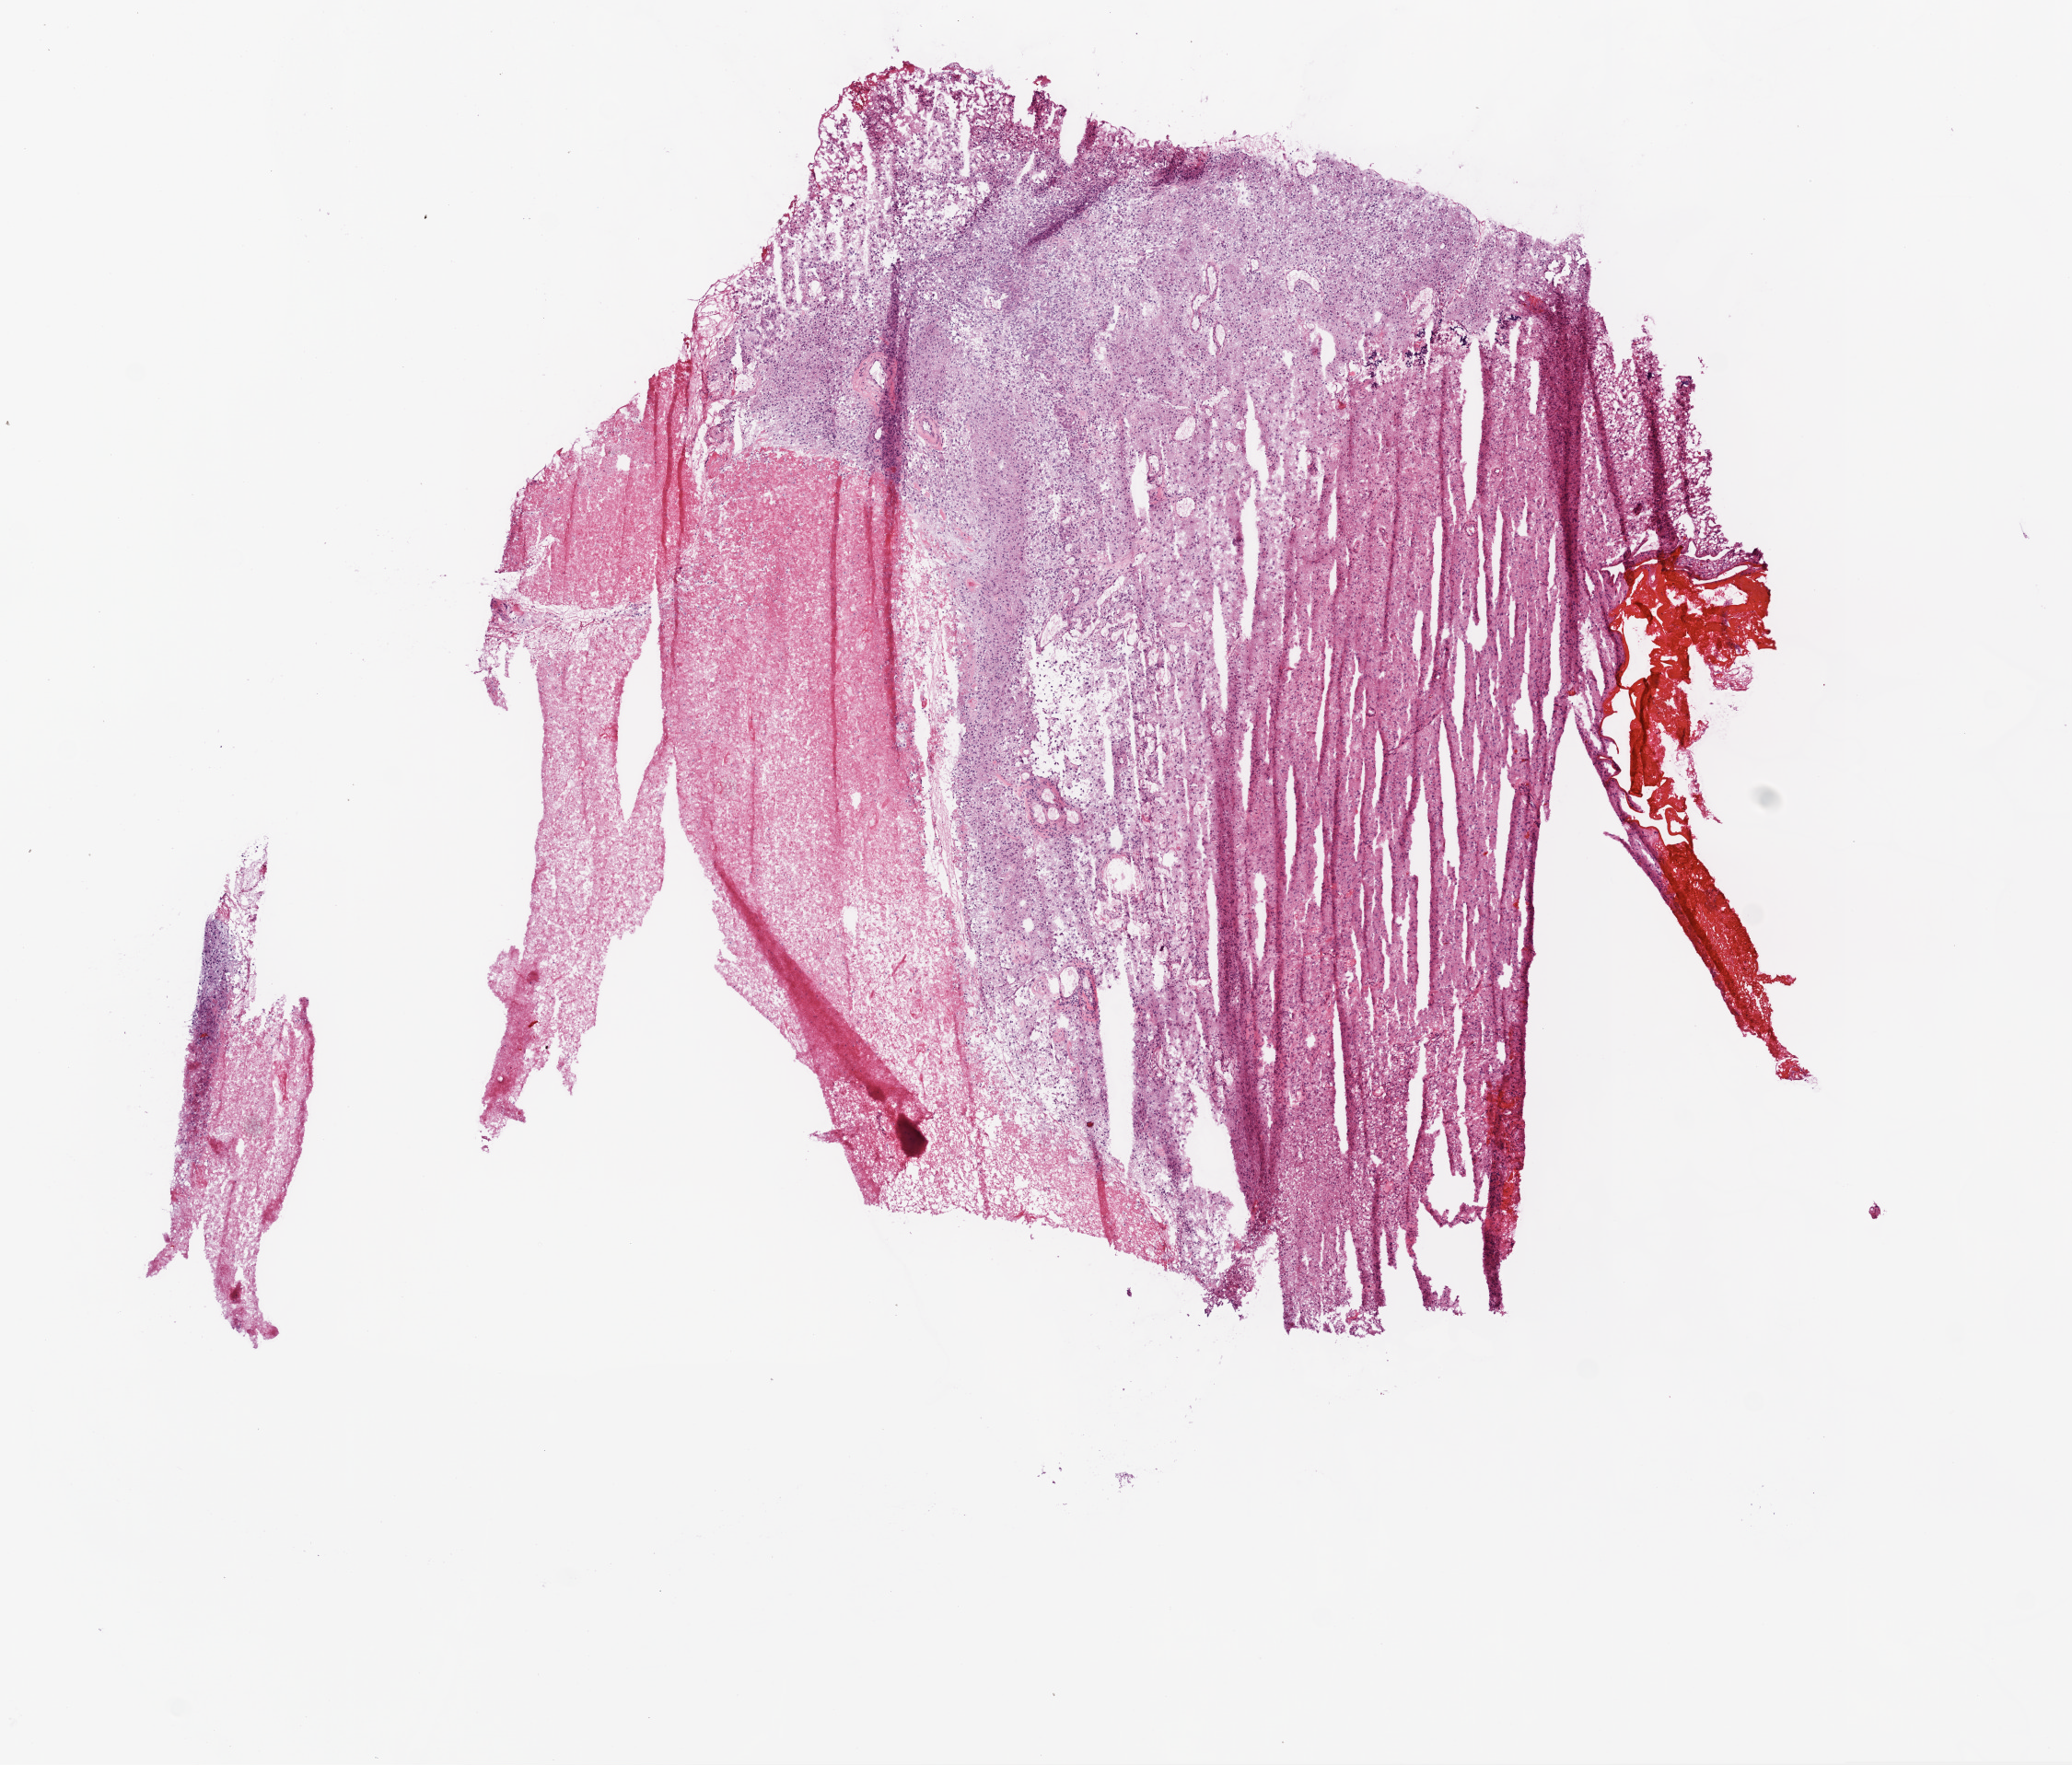
Whole-slide histology image, H&E — a low-resolution overview of the entire scanned area, about 9.0 x 7.7 mm (acquisition: 20x scan), frozen section from the bottom of the tissue portion, primary tumour sample from the brain. Female patient; age at initial diagnosis 63 years. Pathologist review of this section (percent, as recorded): tumour cells 60%, tumour nuclei 85%, normal cells 0%, stromal cells 0%, necrosis 40%.
Diagnosis: Glioblastoma.